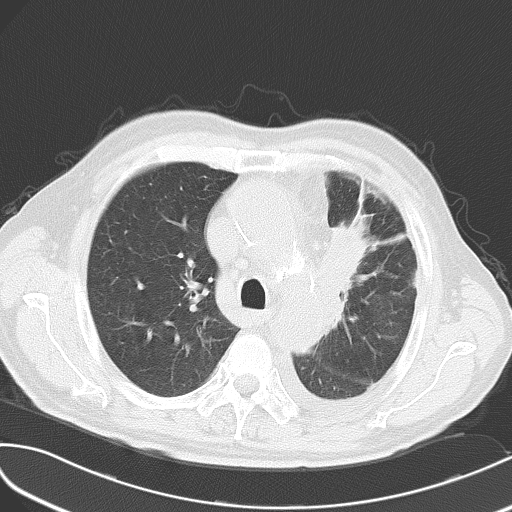
Chest CT, one axial slice; position 39 of 54 along the scan axis; reconstruction kernel B70f; 120 kVp; lung window (W 1500 / L -600 HU); 5 mm slice thickness; 512 × 512 image matrix. Patient: male, 70 years. From the clinical record (not read from this slice): clinical TNM (as recorded): T2 N1 M3.
Outlined on this slice (bounding box drawn by a radiologist):
- lung tumour (recorded histology: small cell carcinoma): box from (x=331, y=216) to (x=380, y=295) px